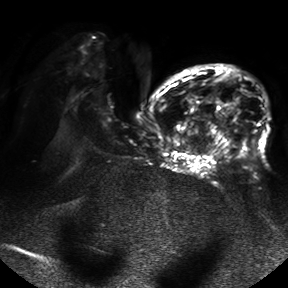
Breast MRI, one axial slice; slice 25 of 50 in the series (ordered by position); diffusion-weighted series; image 2 of 4 stored at this slice position (different b-values; order by instance number); 1.5 T; 288 × 288 image matrix, field of view 390 × 390 mm. Female patient.
Structures marked on this image (manually delineated by an expert):
- tumour on diffusion-weighted imaging: bounding box (x1, y1, x2, y2) in pixels: (228, 102, 236, 113)